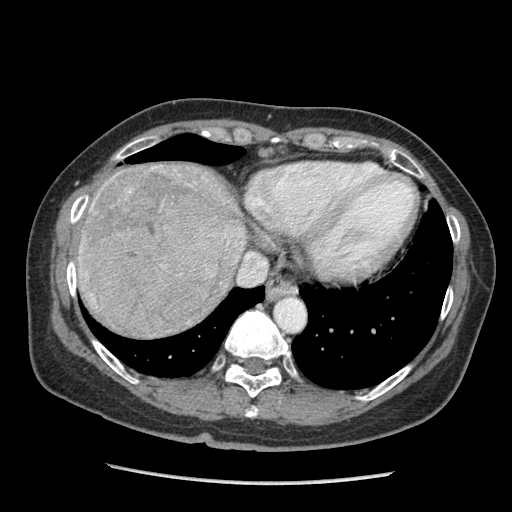
Contrast-enhanced abdominal CT (liver protocol), one axial slice. Position 82 of 105 along the scan axis. Reconstruction kernel STANDARD. 140 kVp. Soft-tissue window (W 400 / L 40 HU). 2.5 mm slice thickness. 512 × 512 image matrix, field of view 340 × 340 mm. Case-level facts recorded for this patient, not image findings: diagnosis: hepatocellular carcinoma (patient treated with transarterial chemoembolisation; whether this scan precedes or follows treatment is not stated here); TNM stage (as recorded): Stage-I; Child-Pugh class: A; tumour differentiation: moderately differentiated; tumour nodularity: uninodular.
Outlined on this slice (semi-automatic segmentation, software-assisted and operator-edited):
- liver parenchyma outside the tumour (the mass and vessels are separate outlines, so this box may not span the whole liver): bounding box <76,164,246,328> (left, top, right, bottom; pixels)
- mass: <79,165,234,338>